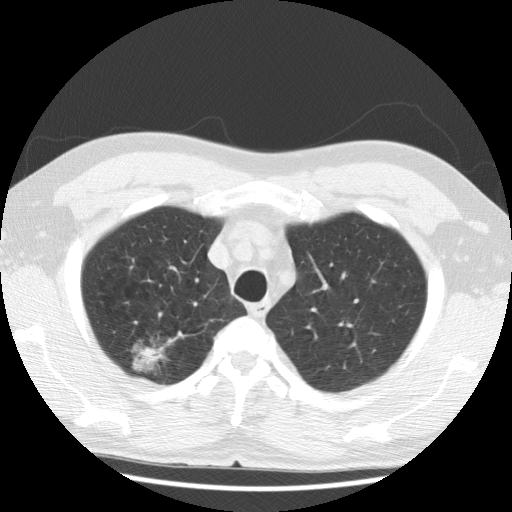
Low-dose screening chest CT, axial slice, baseline screening round, lung window (W 1500 / L -600 HU), standard (soft-tissue) reconstruction kernel (STANDARD), slice 26 of 122 in the series. Male participant, aged 59 years at enrolment. Former smoker at enrolment.
- Lesion marked by an expert reader, bounding box [x1, y1, x2, y2] px = [115, 325, 179, 385].
- Screening reader's record for this exam (one nodule recorded; not confirmed to be the boxed lesion): non-calcified nodule or mass ≥4 mm, right upper lobe, 30 × 28 mm, poorly defined margins, ground glass attenuation.
- Official screen result: positive, change unspecified: nodule(s) >= 4 mm or enlarging nodule(s), mass(es), or other non-specific abnormalities suspicious for lung cancer.
- Later outcome: lung cancer diagnosed 40 days after this screen — bronchiolo-alveolar carcinoma, non-mucinous, right upper lobe, well differentiated (G1), stage IA (AJCC 6th edition), 15 mm at pathology.